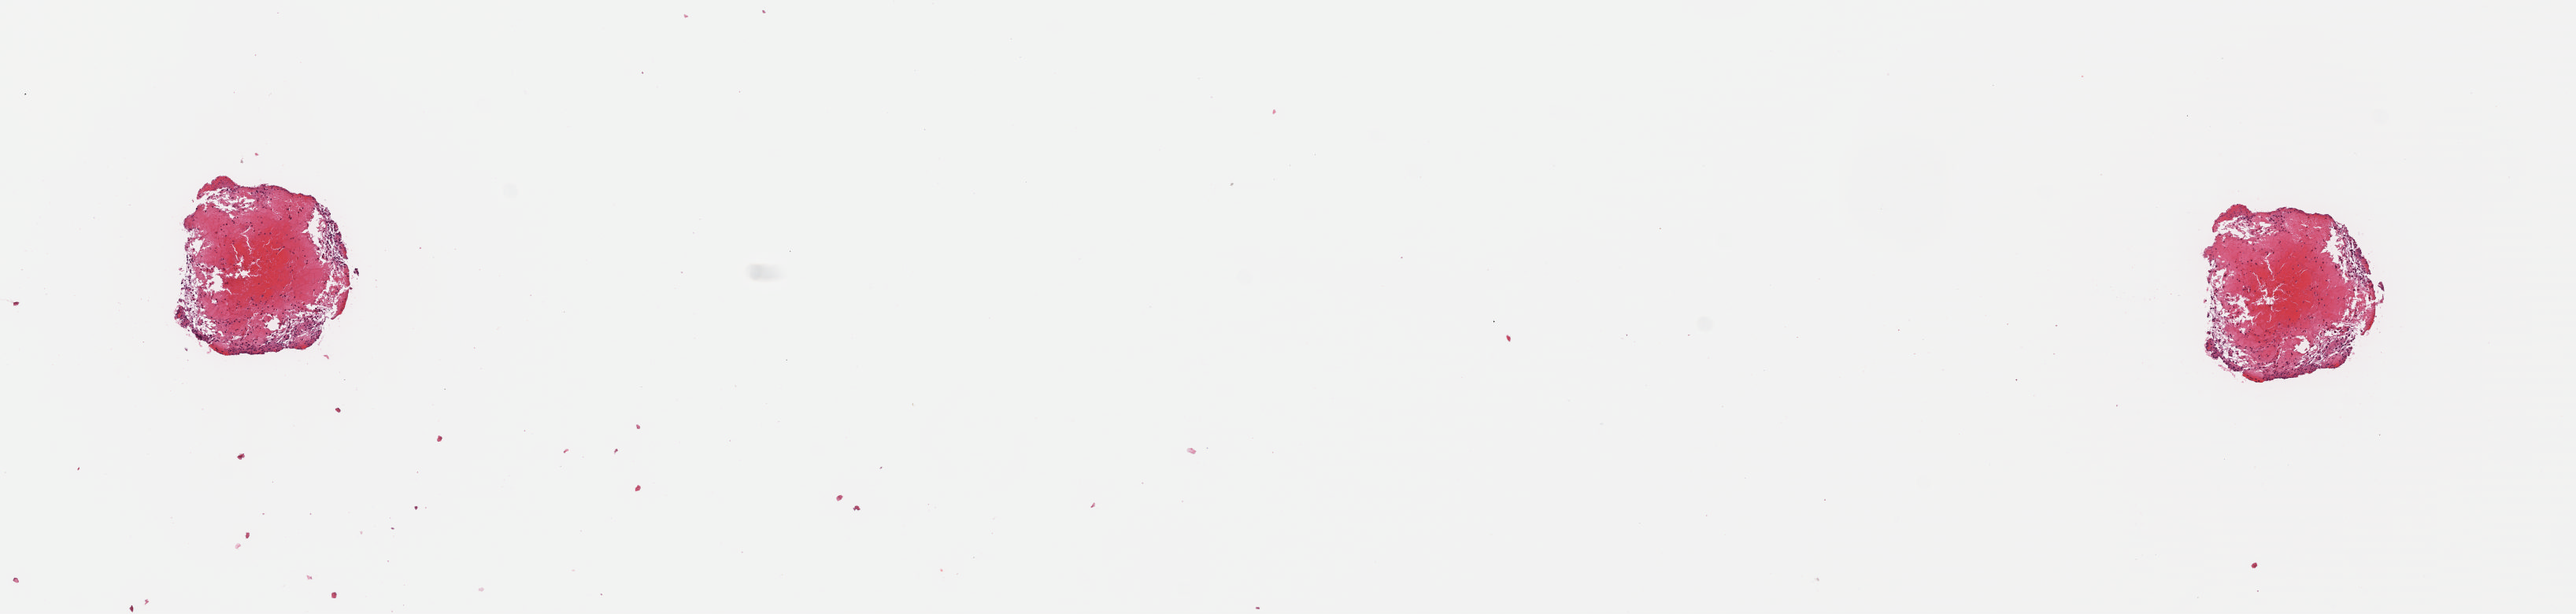
Hematoxylin and eosin (H&E) stained whole-slide image, low-resolution overview of the scanned area, about 12.9 x 3.1 mm (acquisition: 40x scan). FFPE section. Primary tumour sample from the brain. Male patient; age at initial diagnosis 29 years. Histologic grade: G2 (moderately differentiated).
Pathologic diagnosis: Mixed glioma (cerebrum).